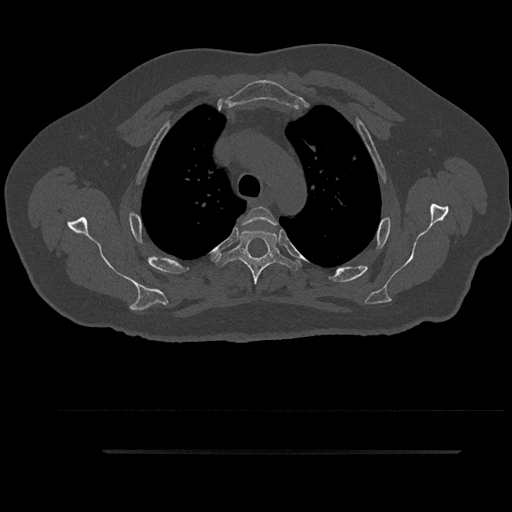
CT including the spine, one axial slice. Reconstruction kernel Br40s/3. Bone window (W 1800 / L 400 HU). 512 × 512 image matrix, field of view 432 × 432 mm. Male patient, age 63 years. From the clinical record (not read from this slice): primary cancer: renal; vertebrae with lytic lesions (as recorded): T8.
Annotated regions visible in this slice (semi-automatic segmentation, software-assisted and operator-edited):
- T3 vertebra: bounding box (x1, y1, x2, y2) in pixels: (242, 207, 277, 226)
- T4 vertebra: (215, 229, 300, 285)